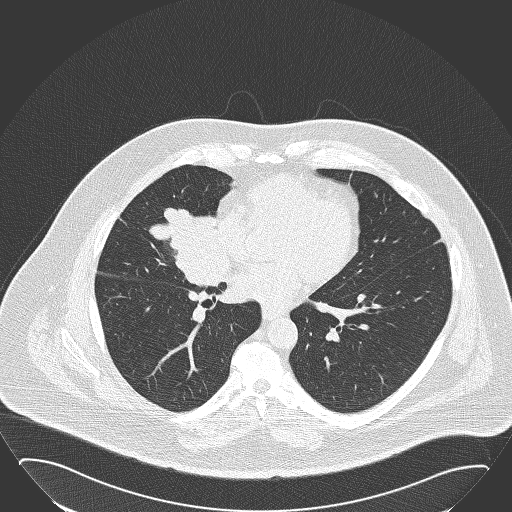
Low-dose screening chest CT, axial slice. First (baseline) screen. Lung window (W 1500 / L -600 HU). 2 mm slice thickness. Lung (sharp) reconstruction kernel (B50f). 120 kVp. Slice 94 of 168 in the series. 512 × 512 image matrix, field of view 432 × 432 mm. Male participant, aged 61 years at enrolment. Former smoker at enrolment.
- Expert-annotated lung lesion, bounding box [x1, y1, x2, y2] px = [142, 194, 229, 281].
- The screening reader recorded 2 non-calcified nodules or masses ≥4 mm on this exam; which of them this box marks is not recorded.
- Lung cancer was diagnosed 47 days after this screen: basaloid squamous cell carcinoma, right middle lobe, right hilum, poorly differentiated (G3), stage IIB (AJCC 6th edition), 95 mm at pathology.